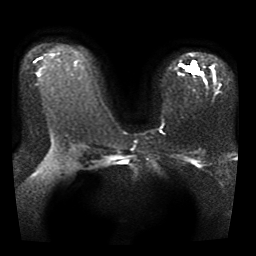
Breast MRI, one axial slice; diffusion-weighted series; image 2 of 4 stored at this slice position (different b-values; order by instance number); 1.5 T; 256 × 256 image matrix, field of view 330 × 330 mm. Female patient.
Structures marked on this image (manually delineated by an expert):
- tumour on diffusion-weighted imaging: bounding box [x1, y1, x2, y2] px = [181, 61, 198, 73]